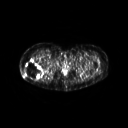
FDG PET of an extremity soft-tissue mass (from a PET/CT study), one axial slice; position 37 of 267 along the scan axis; 3.27 mm slice thickness; 128 × 128 image matrix, field of view 600 × 600 mm. Female patient, age 57 years. Case-level facts recorded for this patient, not image findings: histological type: epithelioid sarcoma with vascular differentiation; site of the primary tumour: right buttock.
Annotated regions visible in this slice (expert contour drawn on MRI and transferred to this co-registered scan by the dataset authors):
- gross tumour volume (mass): bounding box [x1, y1, x2, y2] px = [24, 59, 43, 80]